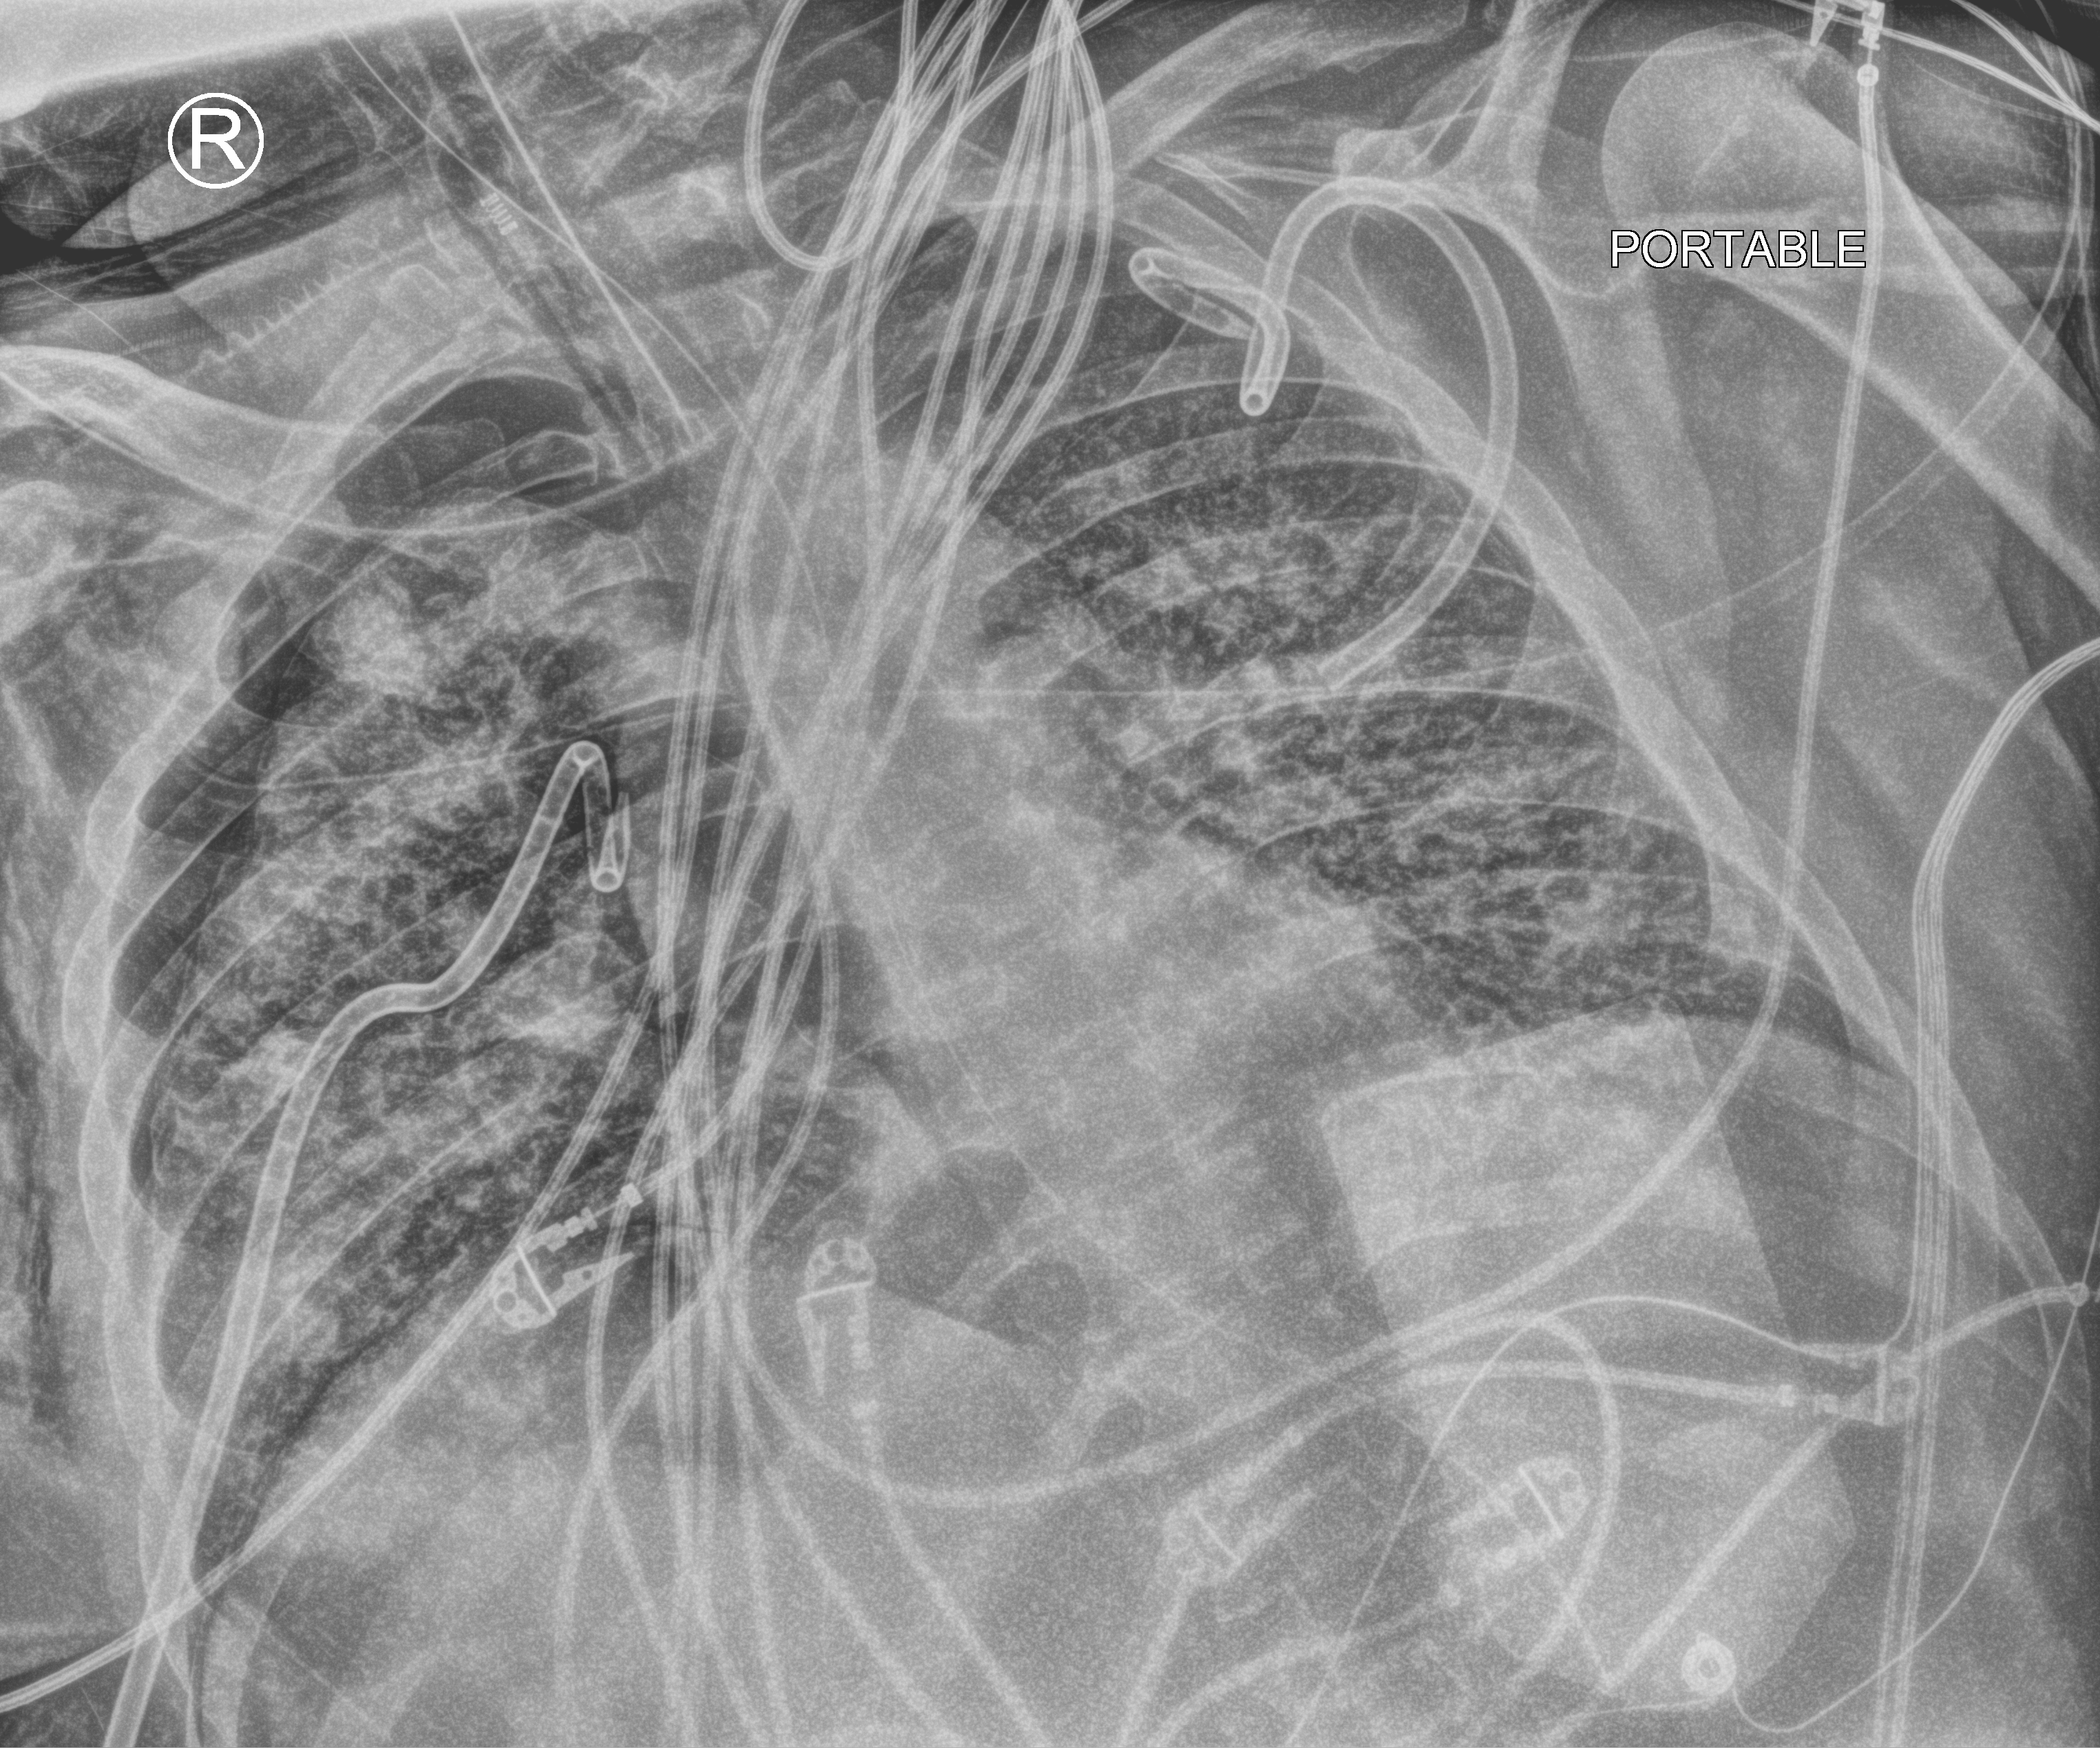
Portable chest radiograph. Adult patient hospitalised with COVID-19, age 18–59 years.
From the hospital-stay record, not from the radiograph (when in the stay this image was taken is not recorded):
- mechanically ventilated during this hospital stay: yes
- length of hospital stay: 31 days
- admitted to intensive care during this hospital stay: yes